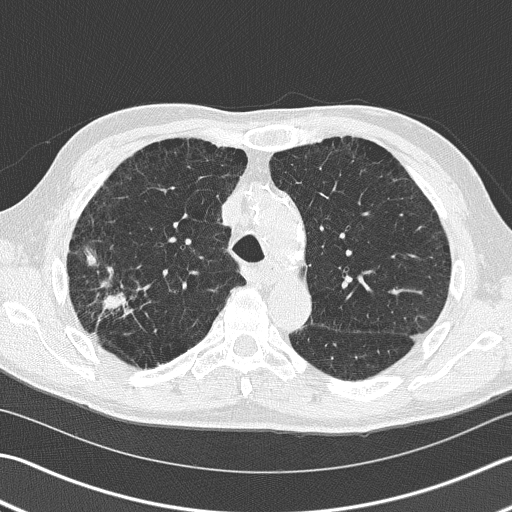
Chest CT (low-dose screening protocol), one axial image, baseline annual screen, lung window (W 1500 / L -600 HU), 2 mm slice thickness, 120 kVp. Male, age 66 years at enrolment. Current smoker at enrolment.
Expert-annotated lung lesion, bounding box <59,240,135,339> (left, top, right, bottom; pixels). Screening reader's record for this exam (one nodule recorded; not confirmed to be the boxed lesion): non-calcified nodule or mass ≥4 mm, right upper lobe, 39 × 23 mm, spiculated (stellate) margins, soft tissue attenuation. Lung cancer was diagnosed 36 days after this screen: squamous cell carcinoma, NOS, right upper lobe, poorly differentiated (G3), stage IB (AJCC 6th edition), 23 mm at pathology.